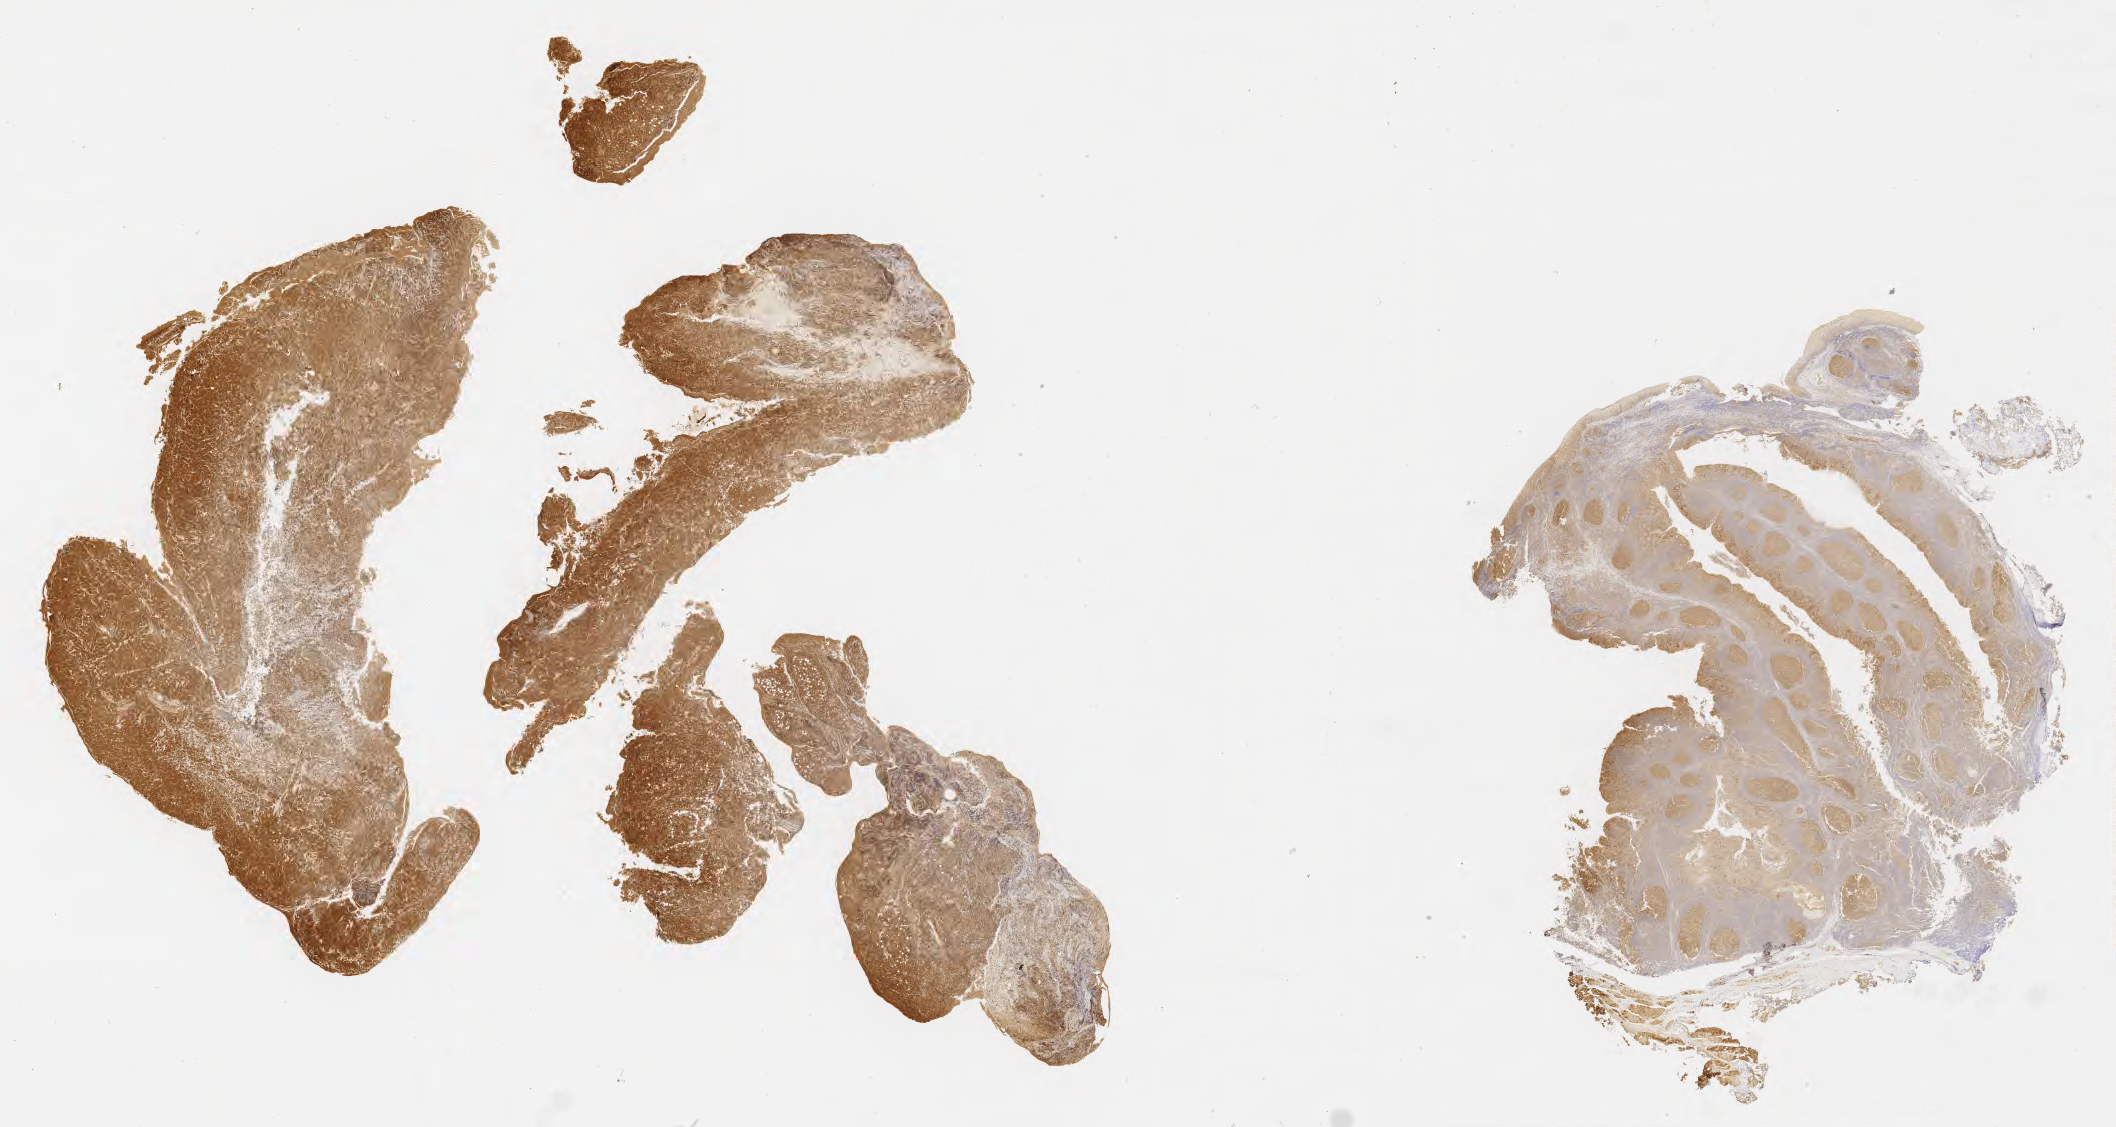
Whole-slide image, immunohistochemical stain for BCL6, low-resolution overview of the scanned area, about 34.2 x 18.2 mm. Tumor tissue. Site: abdomen proper. Male, age 5 years at initial diagnosis.
- histologic diagnosis: Burkitt lymphoma, NOS